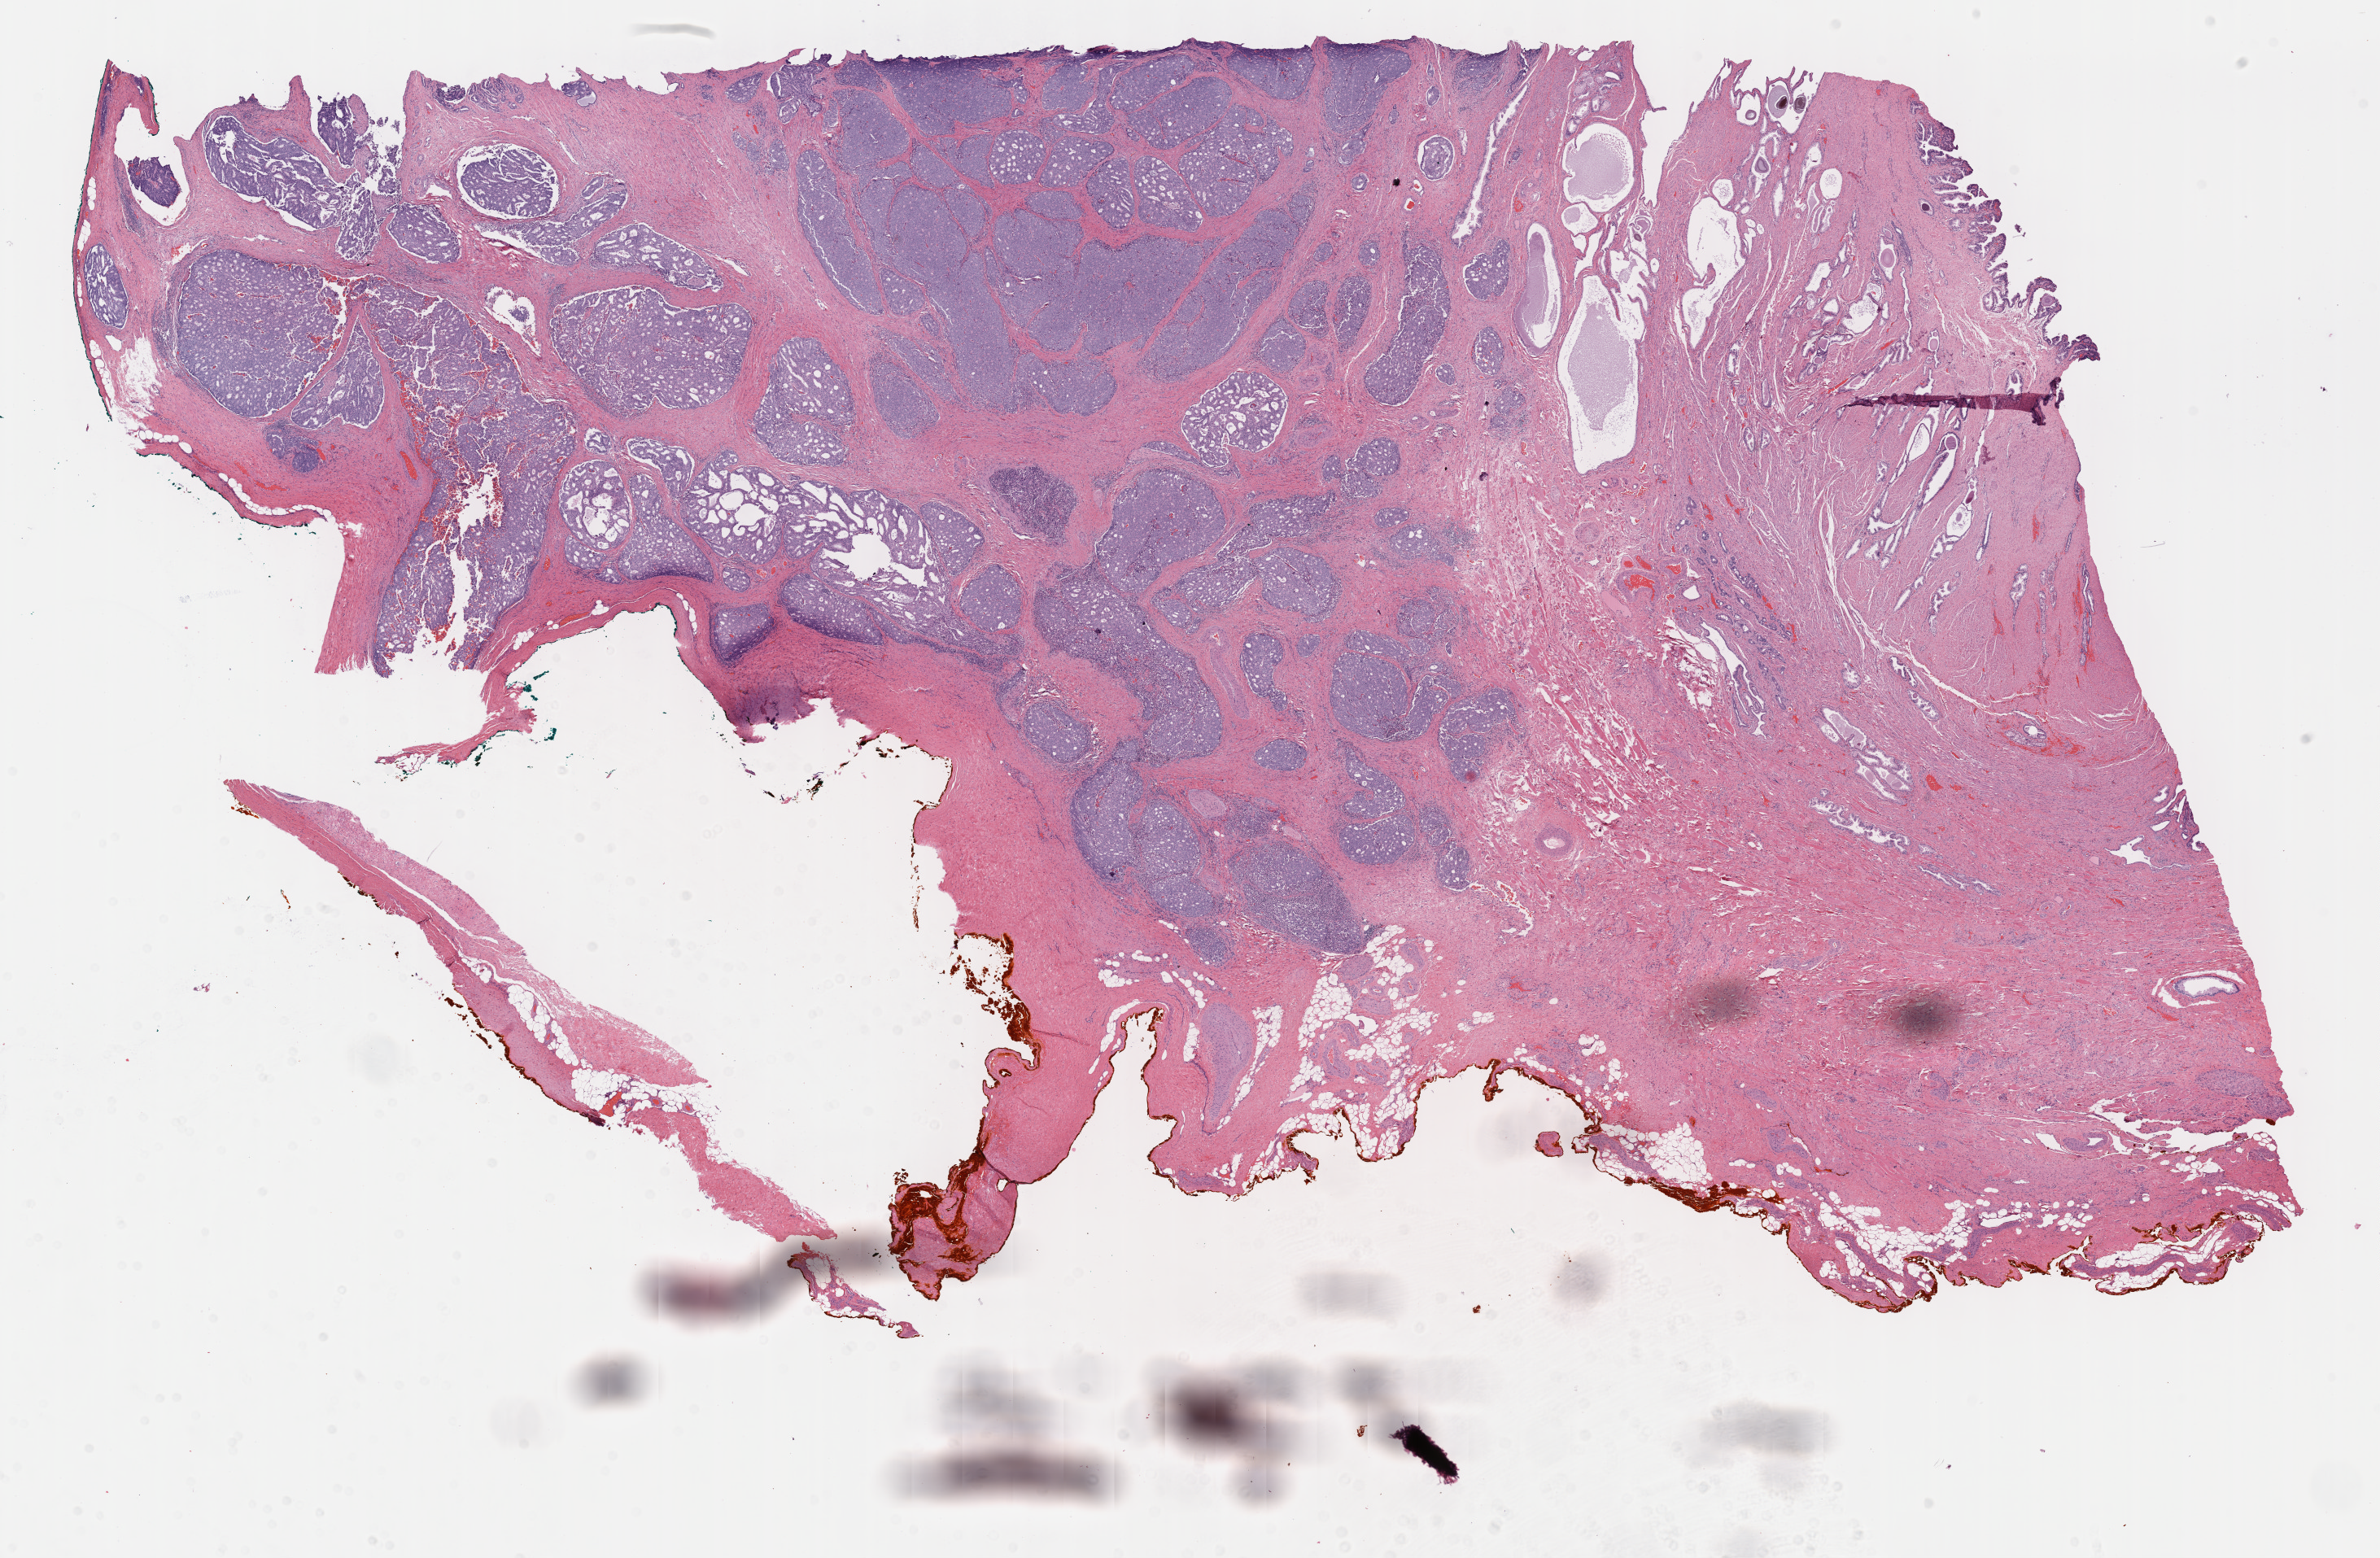
Whole-slide histology image, H&E-stained, whole scanned area (about 23.7 x 15.5 mm, from a 40x scan) shown as a low-resolution overview; FFPE section; sample: primary tumour, prostate. Male, age 55 years at initial diagnosis. Gleason score: 8 (4+4).
Diagnosis: Adenocarcinoma, NOS (prostate gland). Lymph nodes positive (case pathology): 0 of 8 examined.